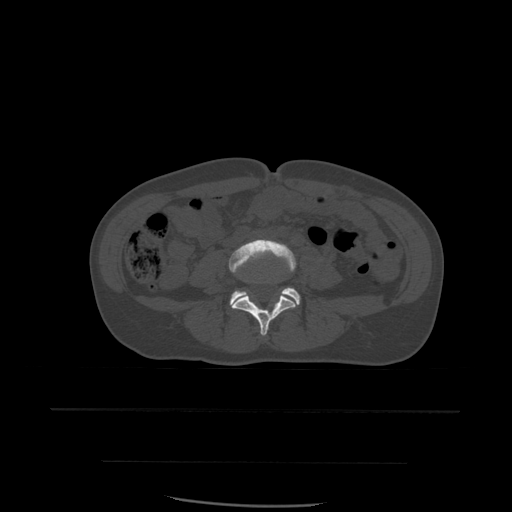
CT including the spine, one axial slice. Position 163 of 574 along the scan axis. Bone window (W 1800 / L 400 HU). 512 × 512 image matrix, field of view 392 × 392 mm. Patient age 48 years. Case-level facts recorded for this patient, not image findings: primary cancer: lung; vertebrae with lytic lesions (as recorded): T11.
Structures marked on this image (semi-automatic segmentation, software-assisted and operator-edited):
- L4 vertebra: box from (x=229, y=239) to (x=298, y=337) px
- L5 vertebra: (x=230, y=288)–(x=301, y=308)